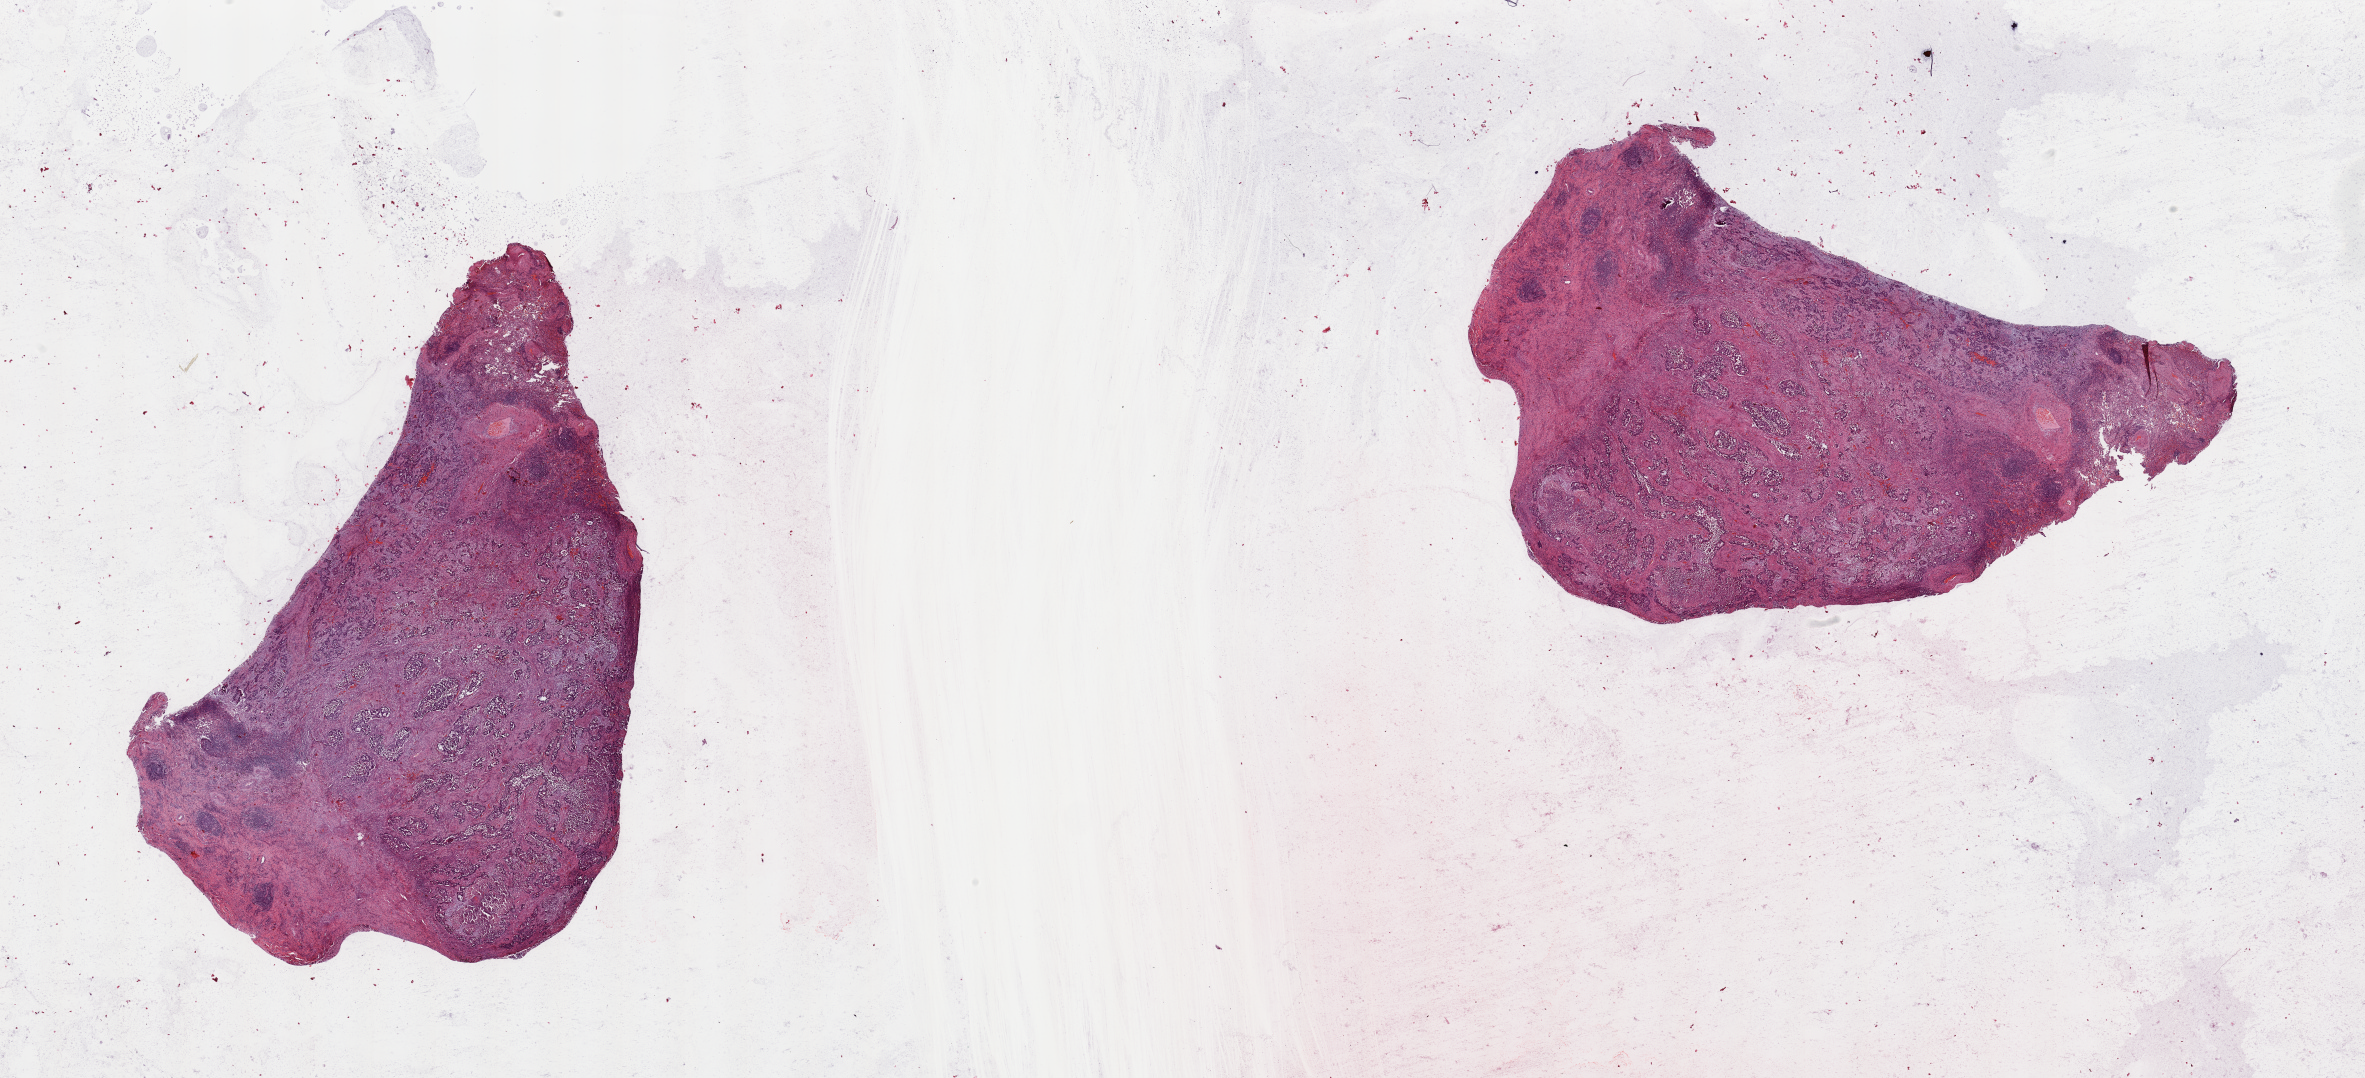
Whole-slide histology image, H&E-stained, whole scanned area (about 37.4 x 17.1 mm, from a 20x scan) shown as a low-resolution overview. Tumour tissue sample, sampled site: lung. Male, 72 y/o. Histologic grade: G3 (poorly differentiated). Composition of this section per pathologist review: tumour nuclei 65%, necrosis 5%.
• histologic diagnosis: Squamous cell carcinoma, NOS
• AJCC pathologic stage: IIIA